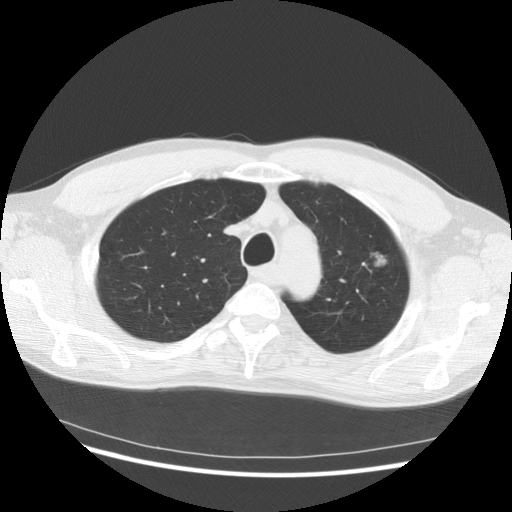
Low-dose screening chest CT, one axial slice; position 113 of 145 along the scan axis; reconstruction kernel STANDARD; 140 kVp; lung window (W 1500 / L -600 HU); 2.5 mm slice thickness; 512 × 512 image matrix, field of view 370 × 370 mm.
Structures marked on this image (outlined manually by an expert reader):
- lesion 1 (tumor, upper lobe of left lung): bounding box <375,256,386,267> (left, top, right, bottom; pixels)